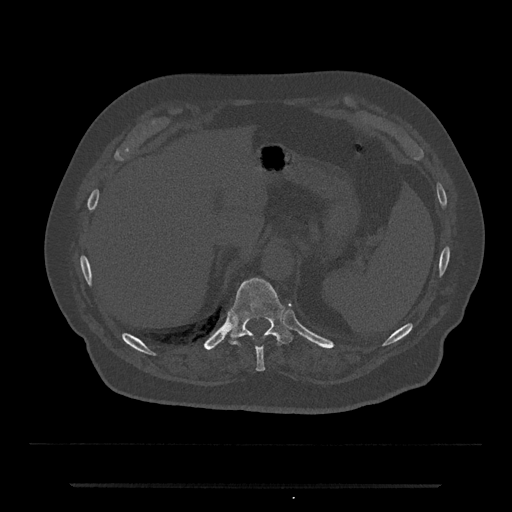
CT including the spine, one axial slice; position 667 of 797 along the scan axis; reconstruction kernel Br40s/3; 120 kVp; bone window (W 1800 / L 400 HU); 0.5 mm slice thickness; 512 × 512 image matrix, field of view 434 × 434 mm. Patient: male, 80 years. Case-level facts recorded for this patient, not image findings: primary cancer: prostate; vertebrae with lytic lesions (as recorded): L1, T11.
Outlined on this slice (semi-automatically segmented with operator editing):
- T10 vertebra: bounding box (x1, y1, x2, y2) in pixels: (256, 347, 265, 372)
- T11 vertebra: (228, 278, 294, 345)